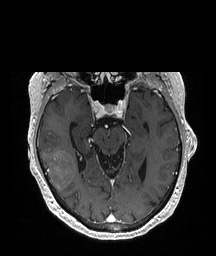
Brain MRI from a brain-tumour surgery series, one axial slice. Slice 129 of 208 in the series (ordered by position). T1-weighted post-contrast. 1 mm slice thickness. 216 × 256 image matrix. Case-level facts recorded for this patient, not image findings: histopathology: Glioblastoma; WHO grade: 4; IDH mutation: no; tumour location: Right Temporal.
Outlined on this slice (expert manual segmentation):
- tumour: bounding box <43,151,76,192> (left, top, right, bottom; pixels)